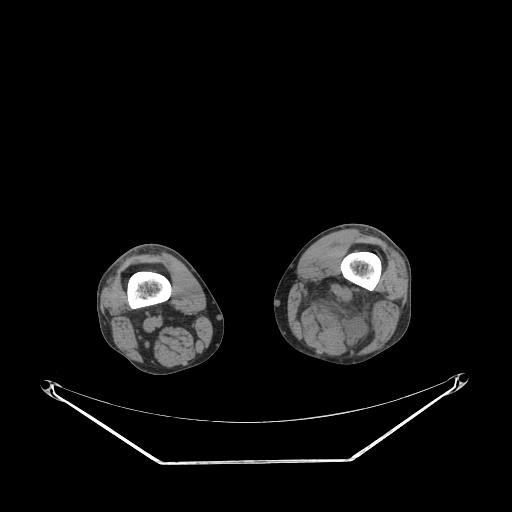
CT of an extremity soft-tissue mass (from a PET/CT study), one axial slice. Position 202 of 267 along the scan axis. Reconstruction kernel STANDARD. Soft-tissue window (W 400 / L 40 HU). 512 × 512 image matrix, field of view 500 × 500 mm. Male patient. Case-level facts recorded for this patient, not image findings: histological type: undifferentiated pleomorphic liposarcoma; grade: high; site of the primary tumour: left thigh.
Structures marked on this image (expert contour drawn on MRI and transferred to this co-registered scan by the dataset authors):
- gross tumour volume including surrounding oedema: box from (x=295, y=278) to (x=382, y=350) px